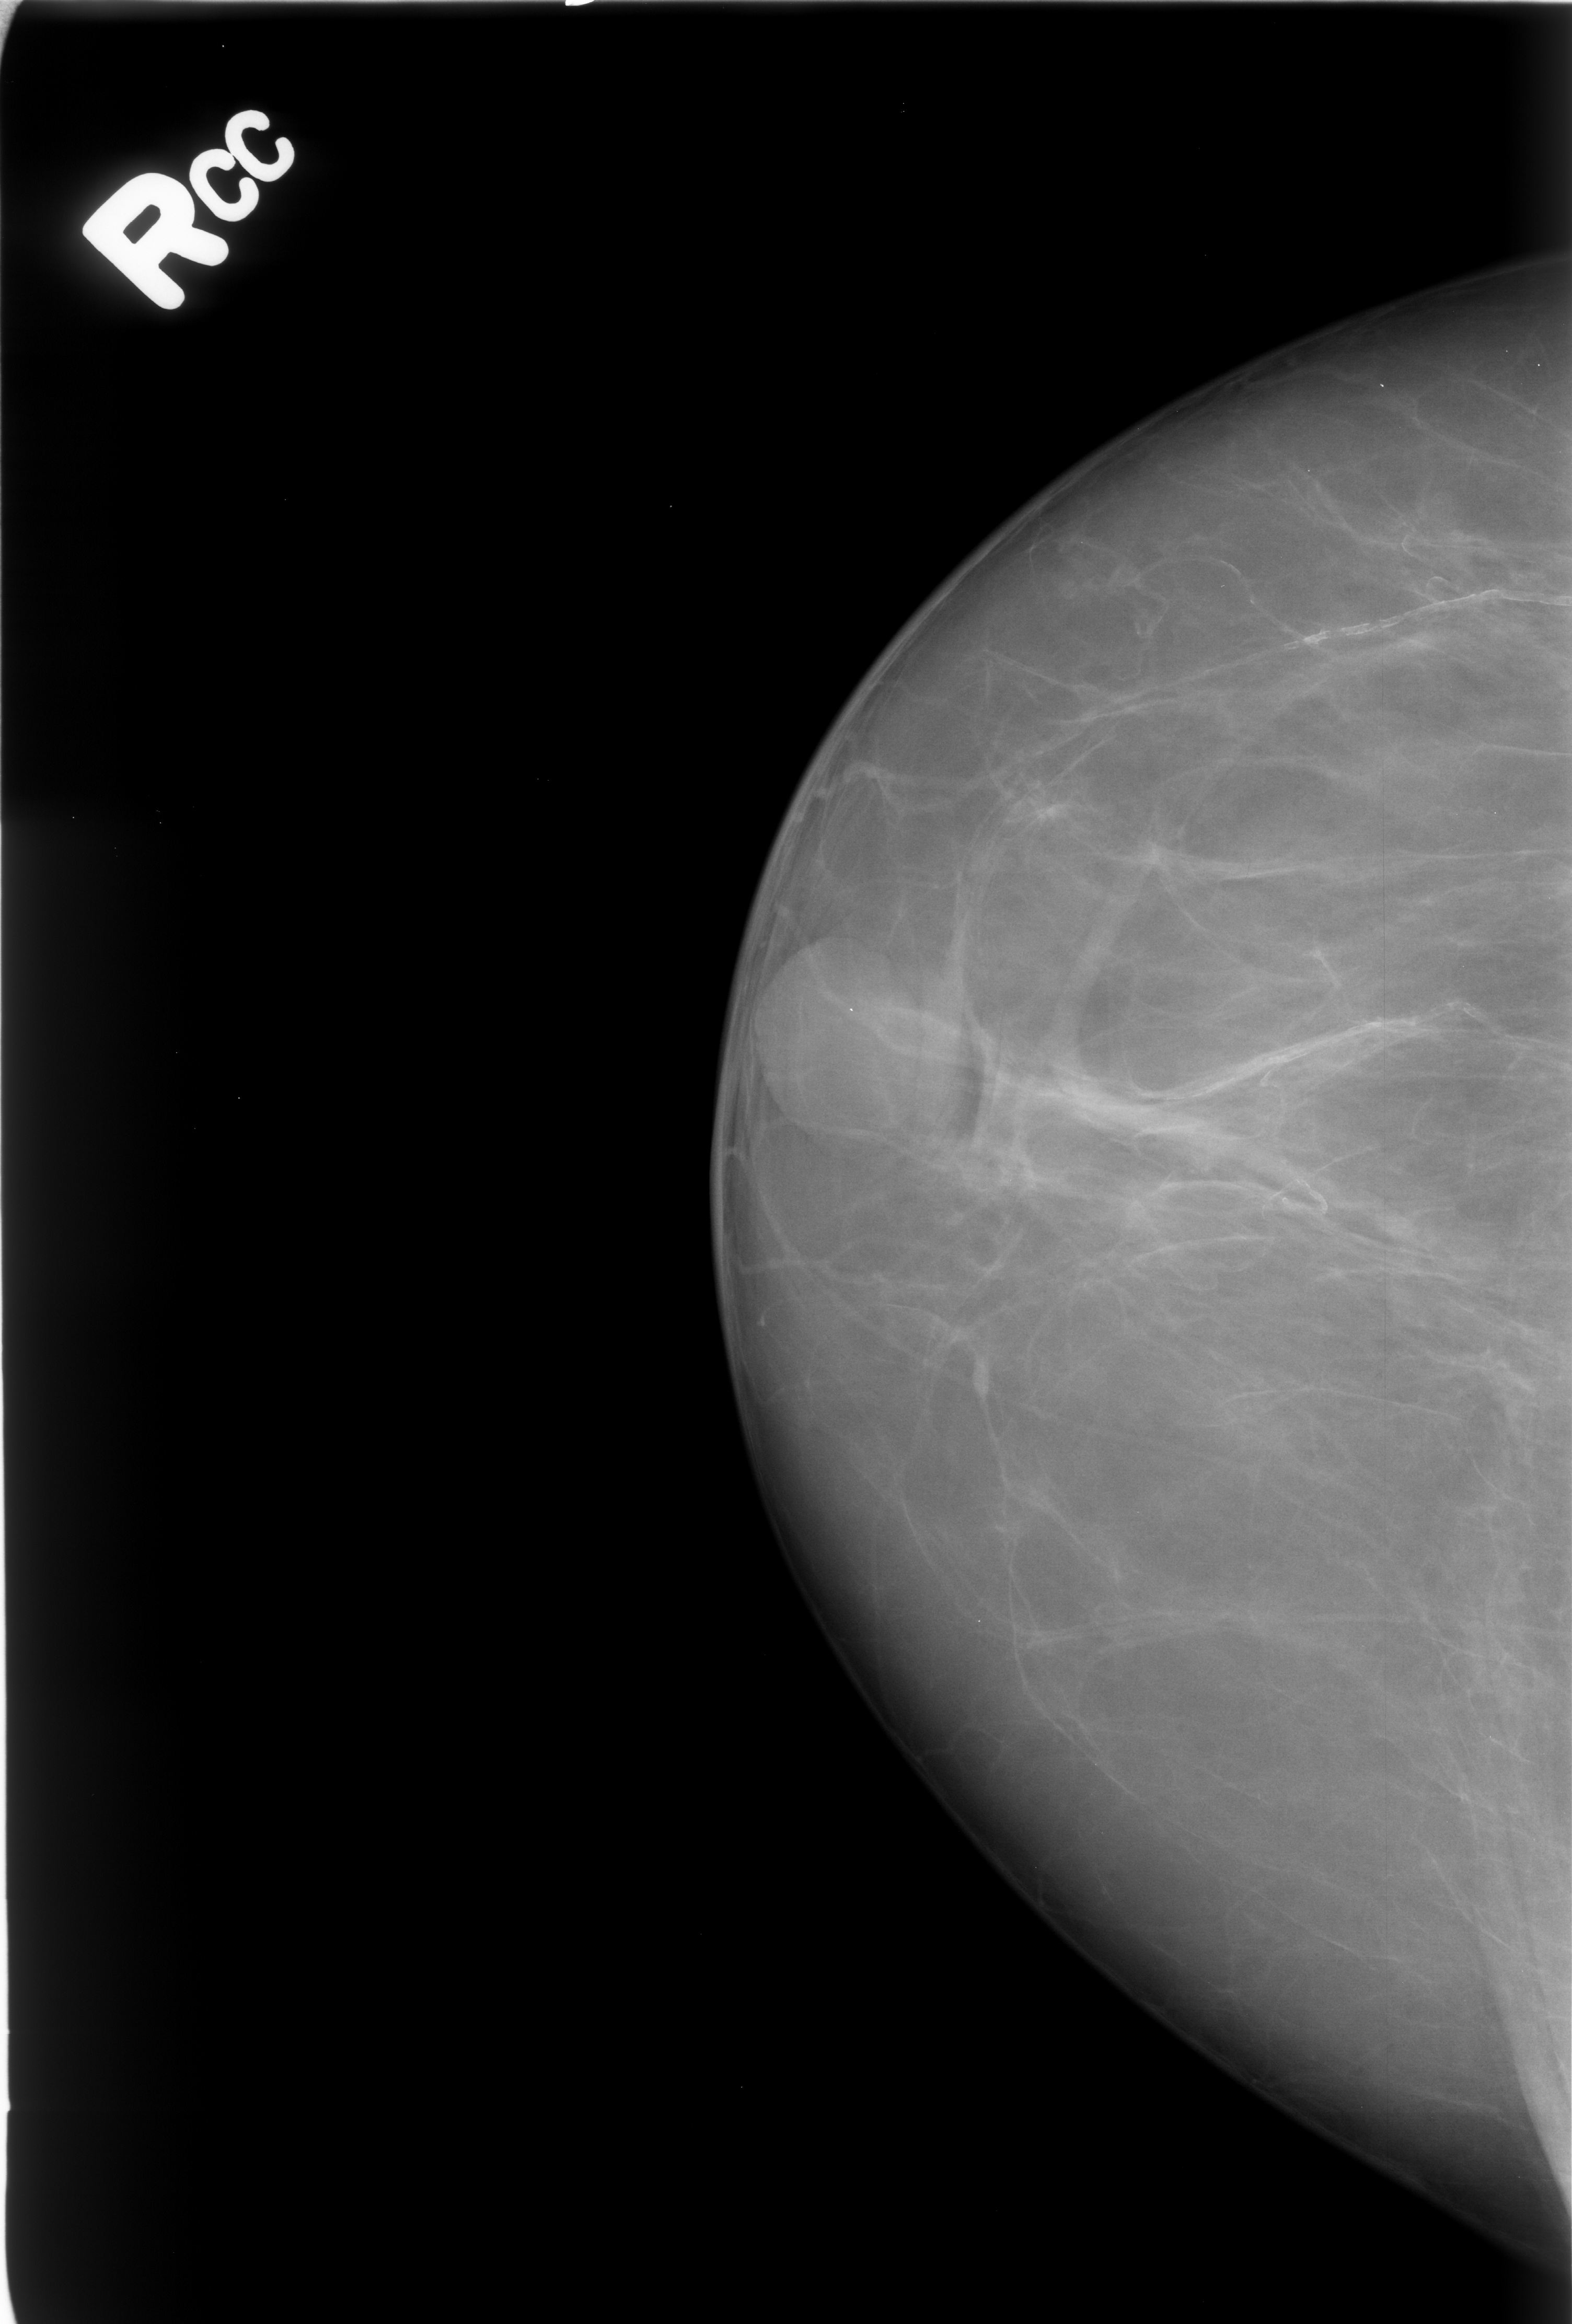
Digitized screen-film mammogram; right breast; CC view; BI-RADS breast density category 1 (scale 1–4); 1572 × 2324 image matrix.
Marked abnormalities (boxes around the expert regions of interest):
- Finding 1 of 2: calcifications, morphology vascular; BI-RADS assessment category 2; subtlety rating 4 on a 1 (subtle) to 5 (obvious) scale; outcome (as recorded, no biopsy): benign without callback (not worked up further): bounding box <903,948,1481,1242> (left, top, right, bottom; pixels)
- Finding 2 of 2: calcifications, morphology vascular; BI-RADS assessment category 2; outcome (as recorded, no biopsy): benign without callback (not worked up further): <1015,589,1460,774>